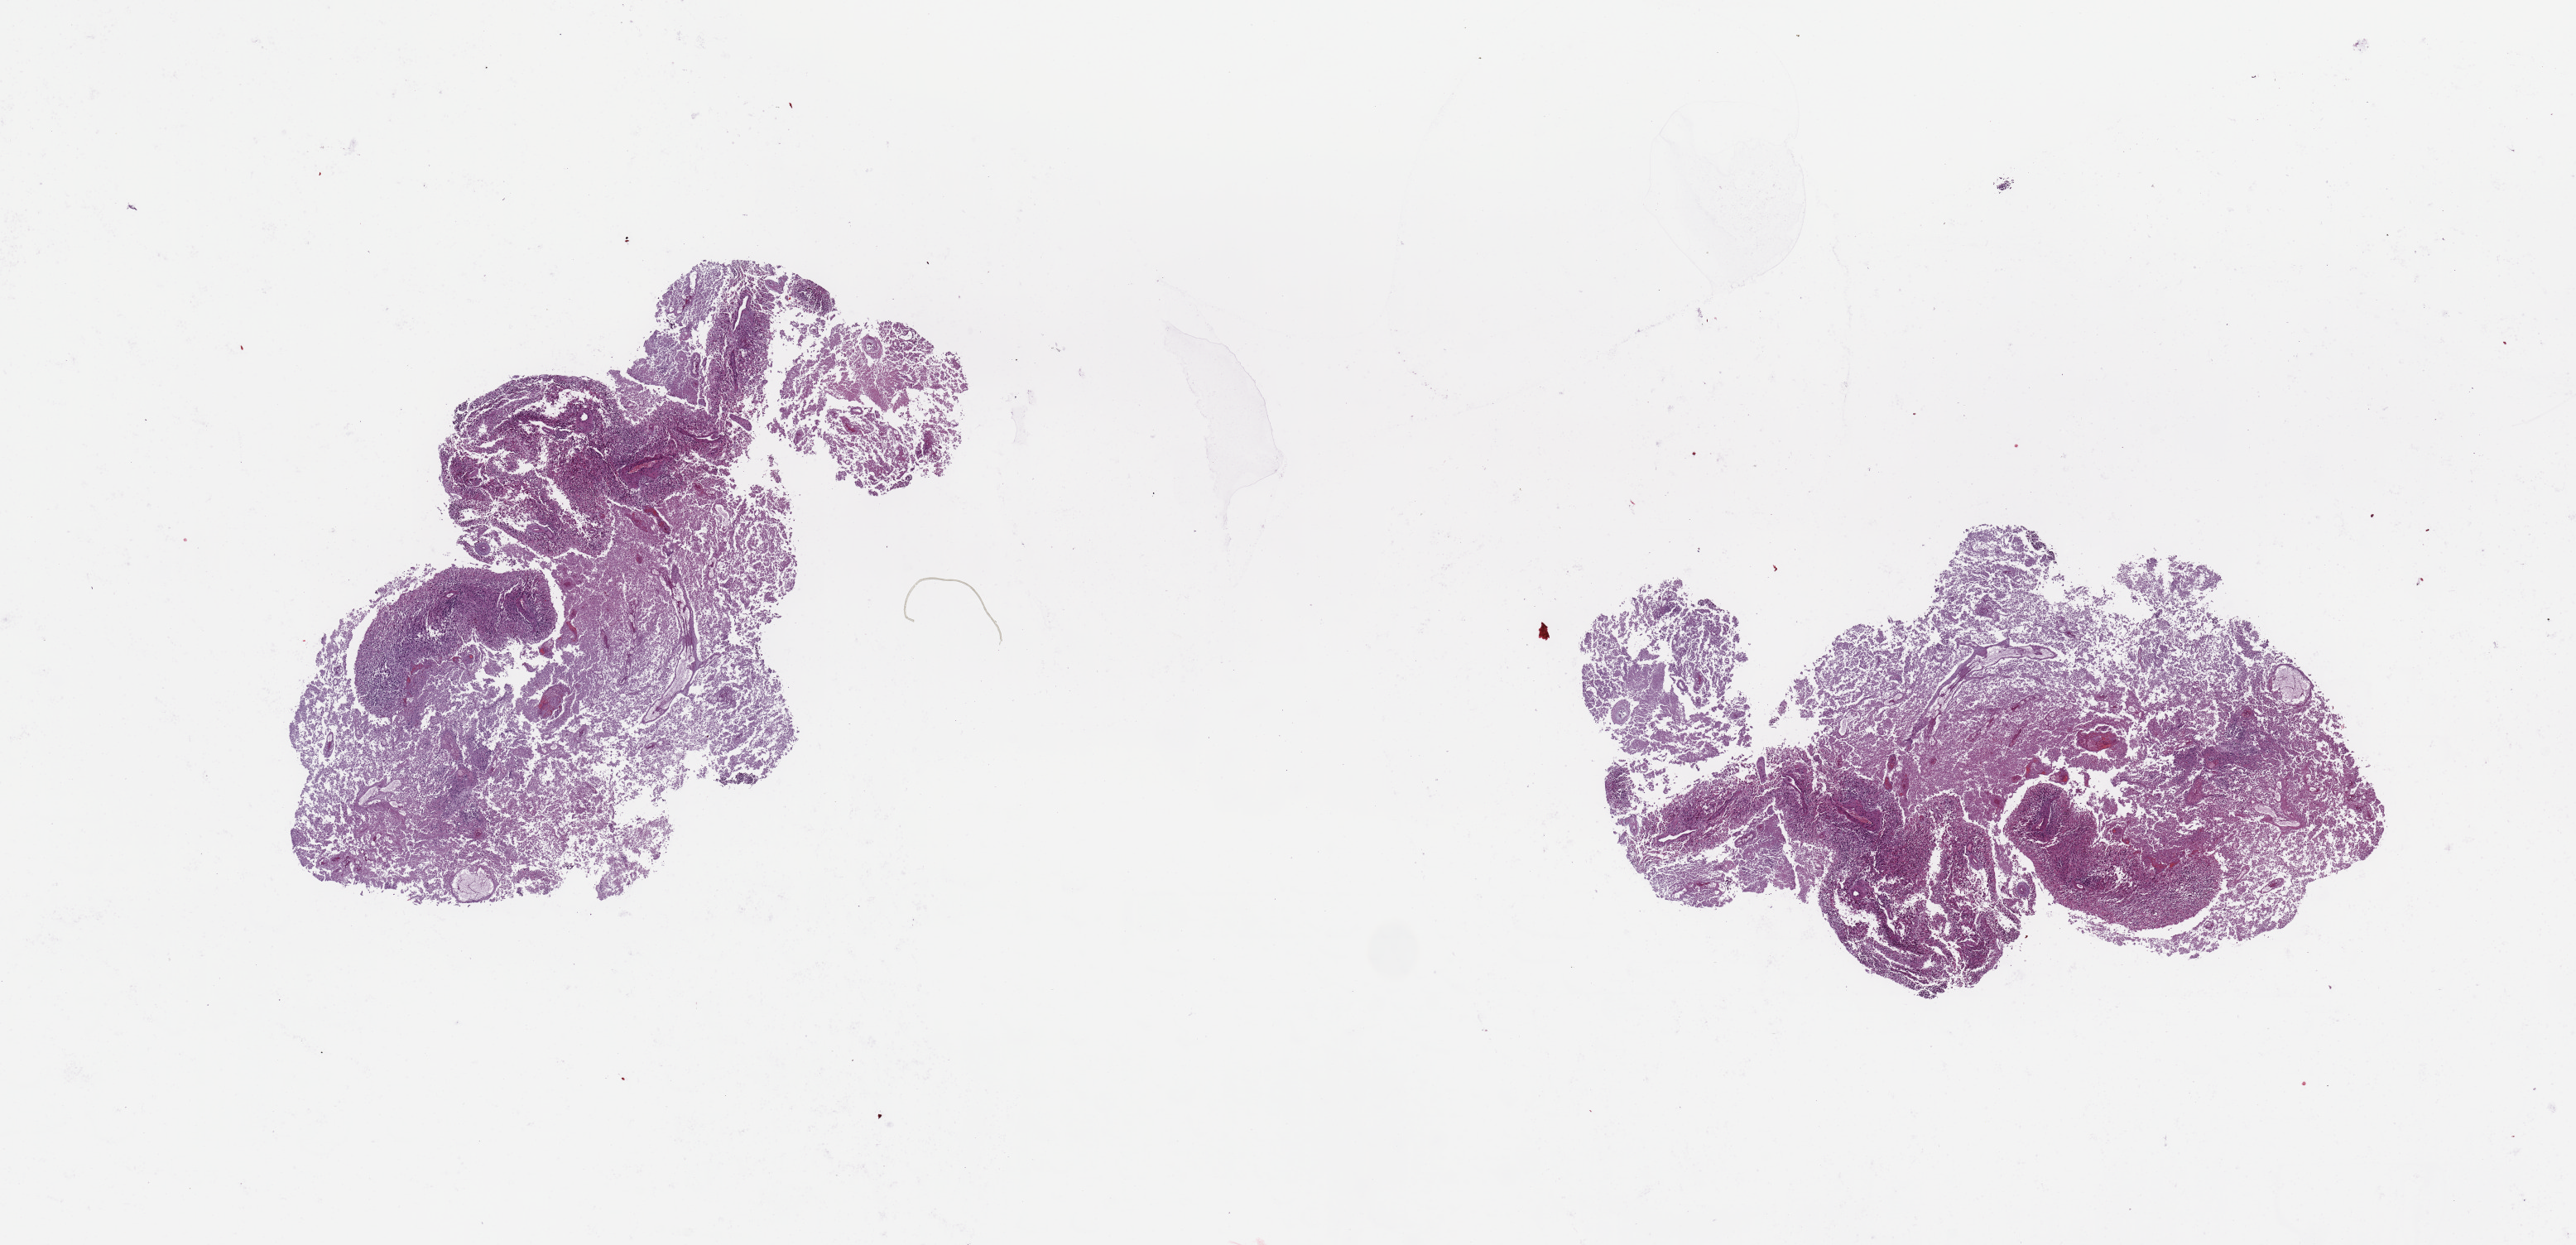
Whole-slide histology image, Hematoxylin and eosin (H&E) stained — whole scanned area (about 24.6 x 11.9 mm, slide scanned at 20x) shown as a low-resolution overview. Brain, tumour tissue. Patient: male, age 53 years.
Diagnosis: Glioblastoma.